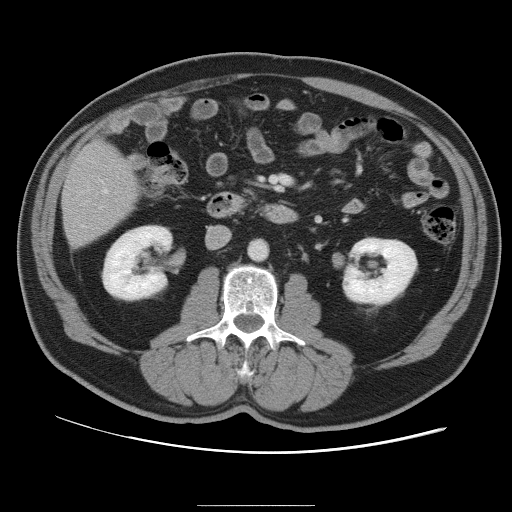
Contrast-enhanced abdominal CT, one axial slice; position 30 of 105 along the scan axis; 120 kVp; intravenous contrast given; soft-tissue window (W 400 / L 40 HU); 512 × 512 image matrix, field of view 399 × 399 mm. Male patient, age 64 years. From the clinical record (not read from this slice): diagnosis: colorectal cancer liver metastases, imaged before liver resection; multiple liver metastases: yes; largest metastasis: 3 cm; disease in both lobes: yes.
Outlined on this slice (manually delineated by an expert):
- hepatic veins: box from (x=104, y=190) to (x=108, y=193) px
- liver: (x=64, y=145)–(x=136, y=246)
- planned liver remnant (the part of the liver to remain after resection): (x=64, y=145)–(x=135, y=231)